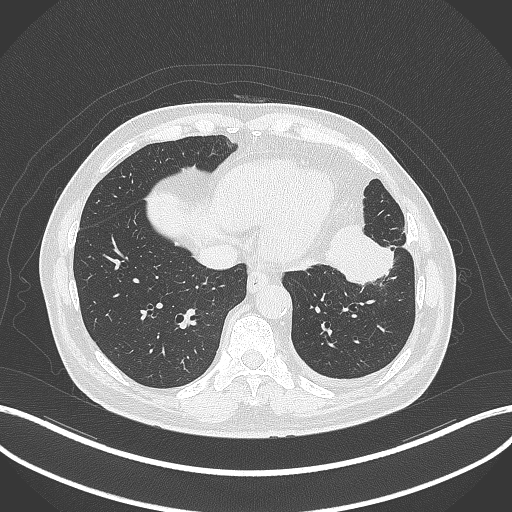
Chest CT, one axial slice. Slice 101 of 230 in the series (ordered by position). 120 kVp. Lung window (W 1500 / L -600 HU). 1 mm slice thickness. 512 × 512 image matrix, field of view 400 × 400 mm. Patient: male, 68 years. From the clinical record (not read from this slice): clinical TNM (as recorded): T2b N0 M0.
Structures marked on this image (rectangle marked by the reading radiologist):
- lung tumour (recorded histology: squamous cell carcinoma): bounding box <322,218,402,293> (left, top, right, bottom; pixels)